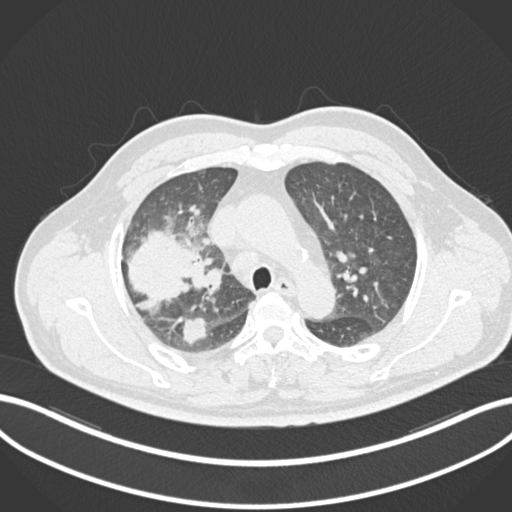
Chest CT, one axial slice. Position 664 of 852 along the scan axis. Reconstruction kernel B30f. Lung window (W 1500 / L -600 HU). 1 mm slice thickness. 512 × 512 image matrix, field of view 400 × 400 mm. Male patient, age 55 years. From the clinical record (not read from this slice): clinical TNM (as recorded): T3 N2 M1.
Outlined on this slice (bounding box drawn by a radiologist):
- lung tumour (recorded histology: adenocarcinoma): bounding box [x1, y1, x2, y2] px = [126, 227, 208, 313]